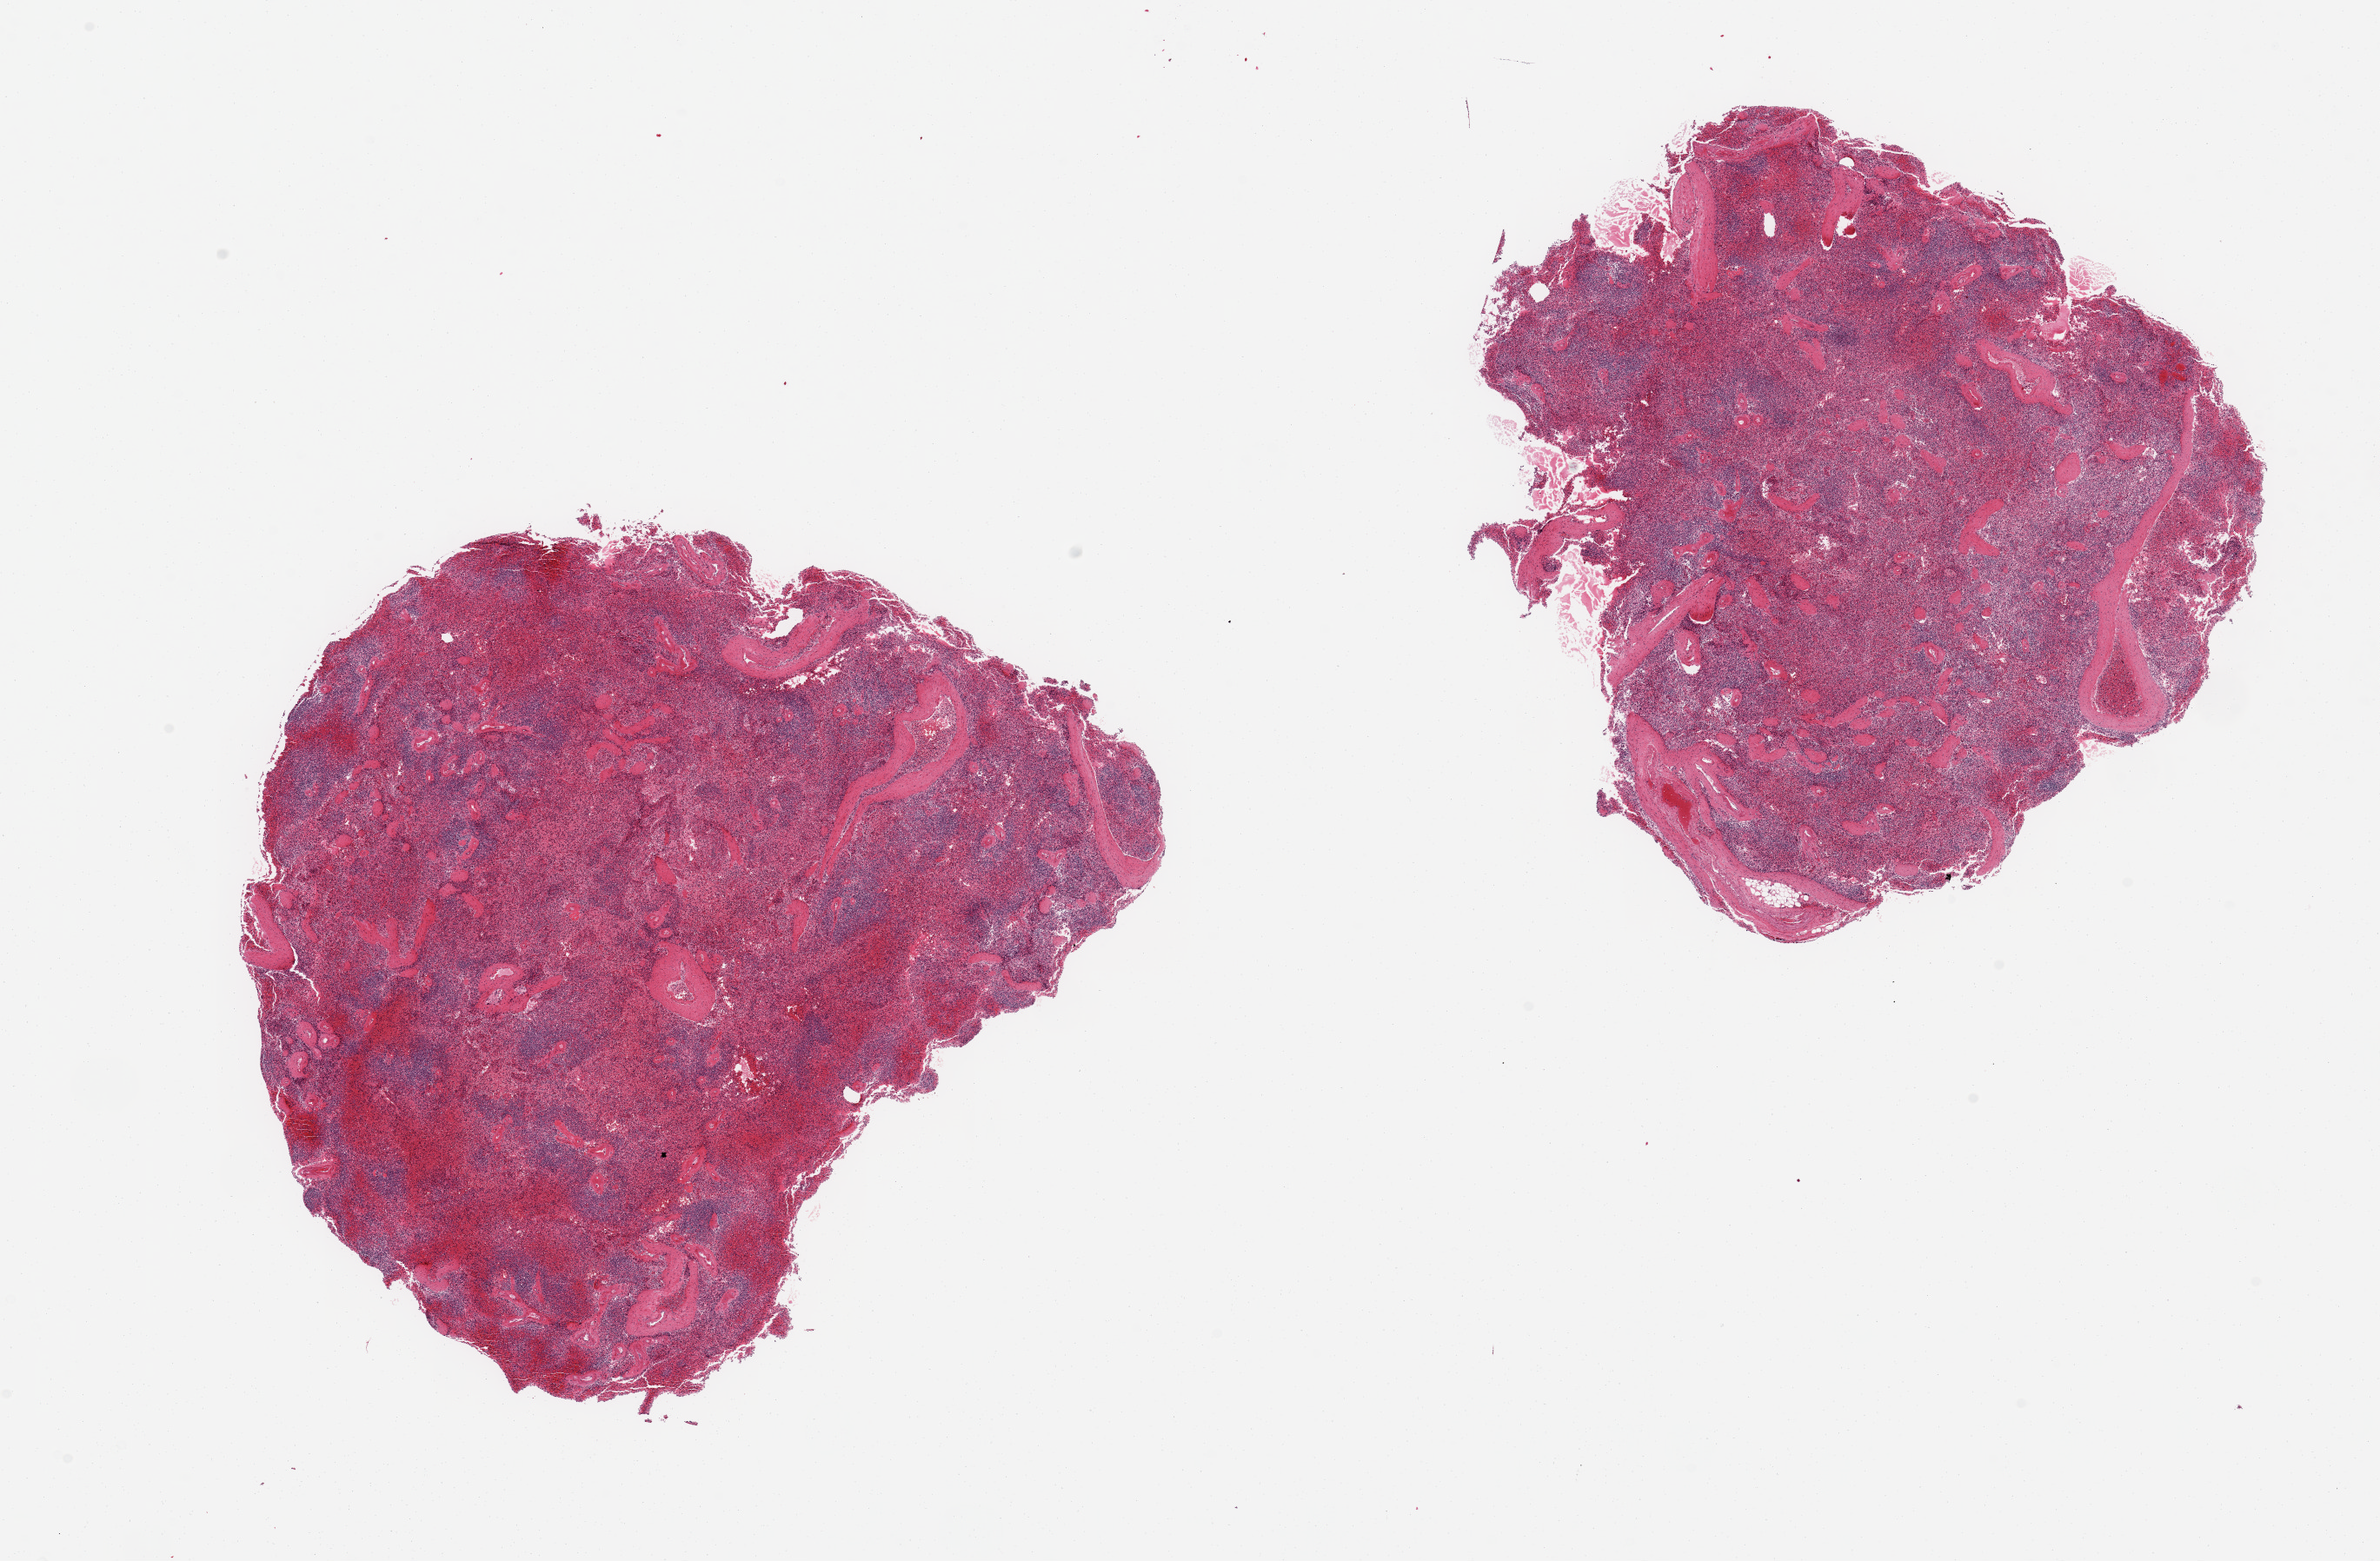
Haematoxylin and eosin whole-slide image, brightfield — low-resolution overview of the scanned area, about 21.7 x 14.2 mm (from a 20x scan), PAXgene-fixed, paraffin-embedded tissue, sampled site (target tissue): spleen, tissue donor sample.
Review note (as recorded): 2 pieces, 7x6 & 8x7 mm.